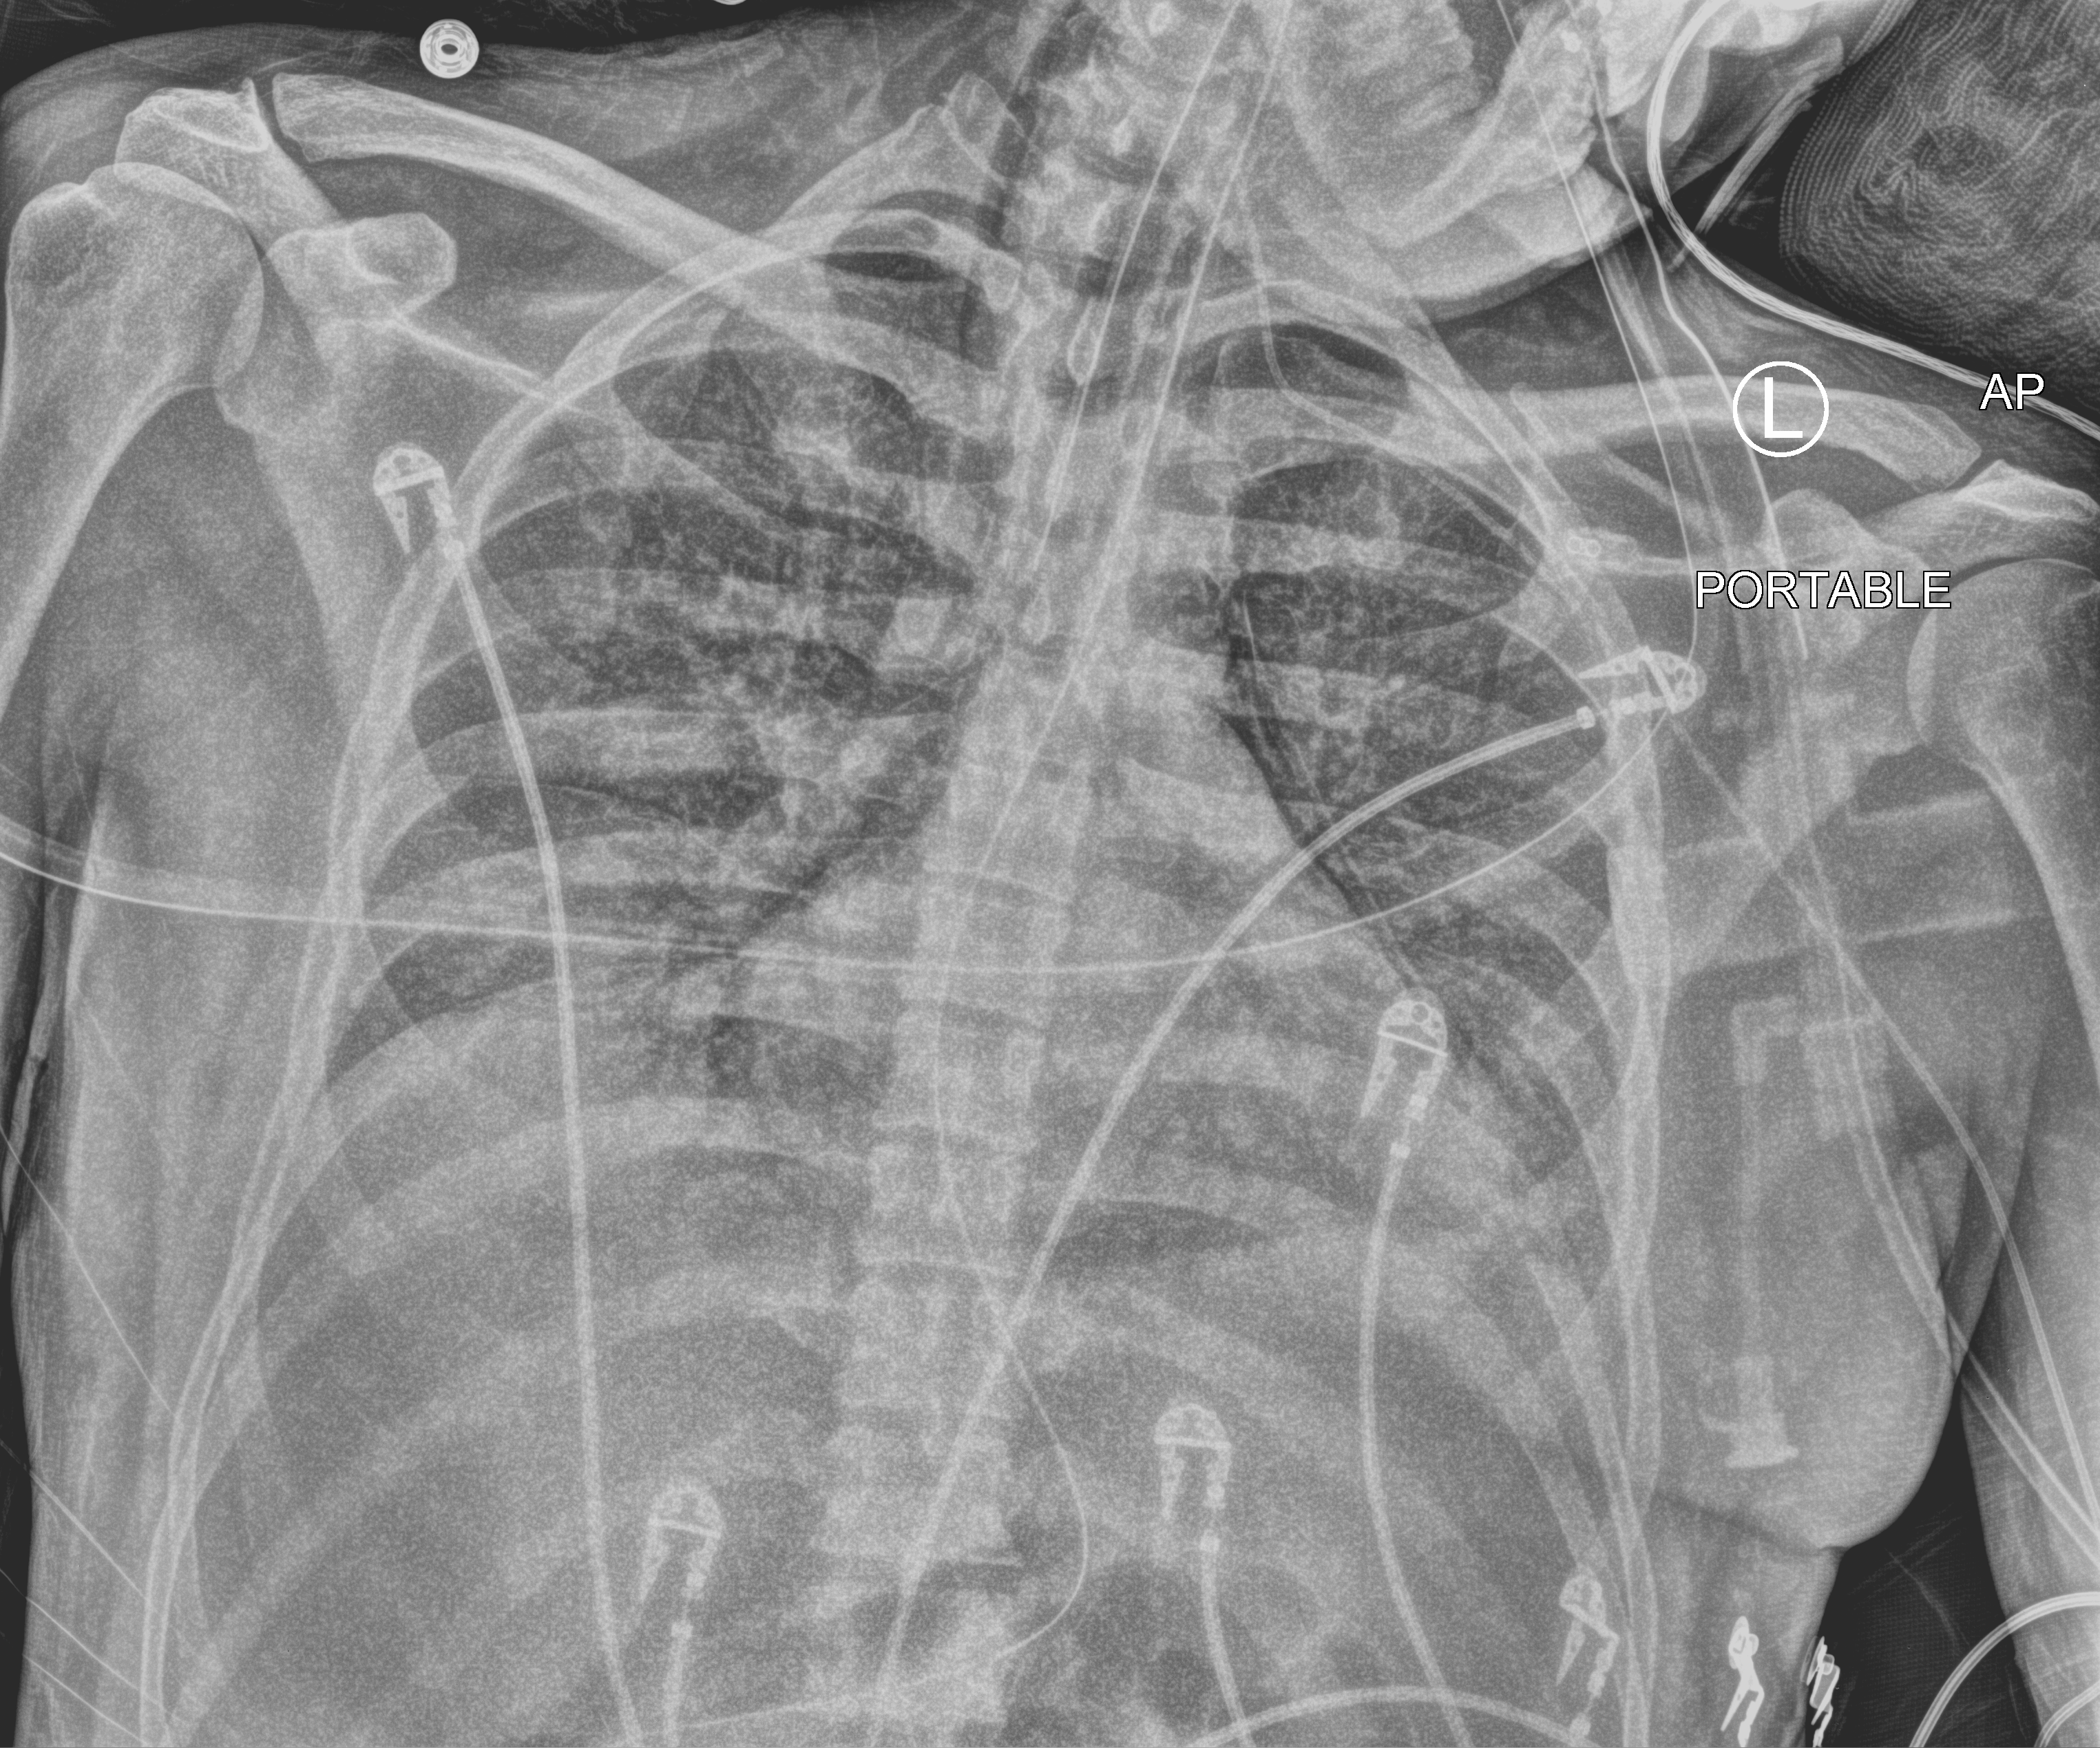
Bedside chest radiograph (computed radiography); anteroposterior (AP) projection. Male patient hospitalised with COVID-19, age 18–59 years.
Admission-level facts for this patient (not findings on this image; timing relative to this image not recorded): admitted to intensive care during this hospital stay: yes.